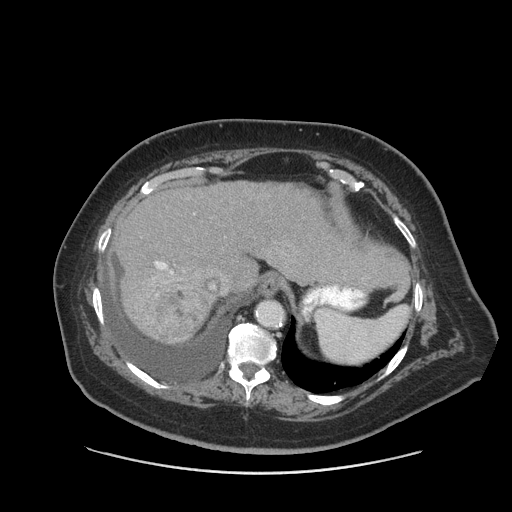
Contrast-enhanced abdominal CT (liver protocol), one axial slice; slice 66 of 91 in the series (ordered by position); reconstruction kernel STANDARD; 140 kVp; soft-tissue window (W 400 / L 40 HU); 512 × 512 image matrix, field of view 420 × 420 mm. Case-level facts recorded for this patient, not image findings: diagnosis: hepatocellular carcinoma (patient treated with transarterial chemoembolisation; whether this scan precedes or follows treatment is not stated here); TNM stage (as recorded): Stage-I; Child-Pugh class: A; tumour nodularity: uninodular.
Annotated regions visible in this slice (semi-automatically segmented with operator editing):
- liver parenchyma outside the tumour (the mass and vessels are separate outlines, so this box may not span the whole liver): bounding box (x1, y1, x2, y2) in pixels: (114, 180, 350, 344)
- mass: (148, 289, 209, 341)
- liver vessels: (155, 261, 173, 274)